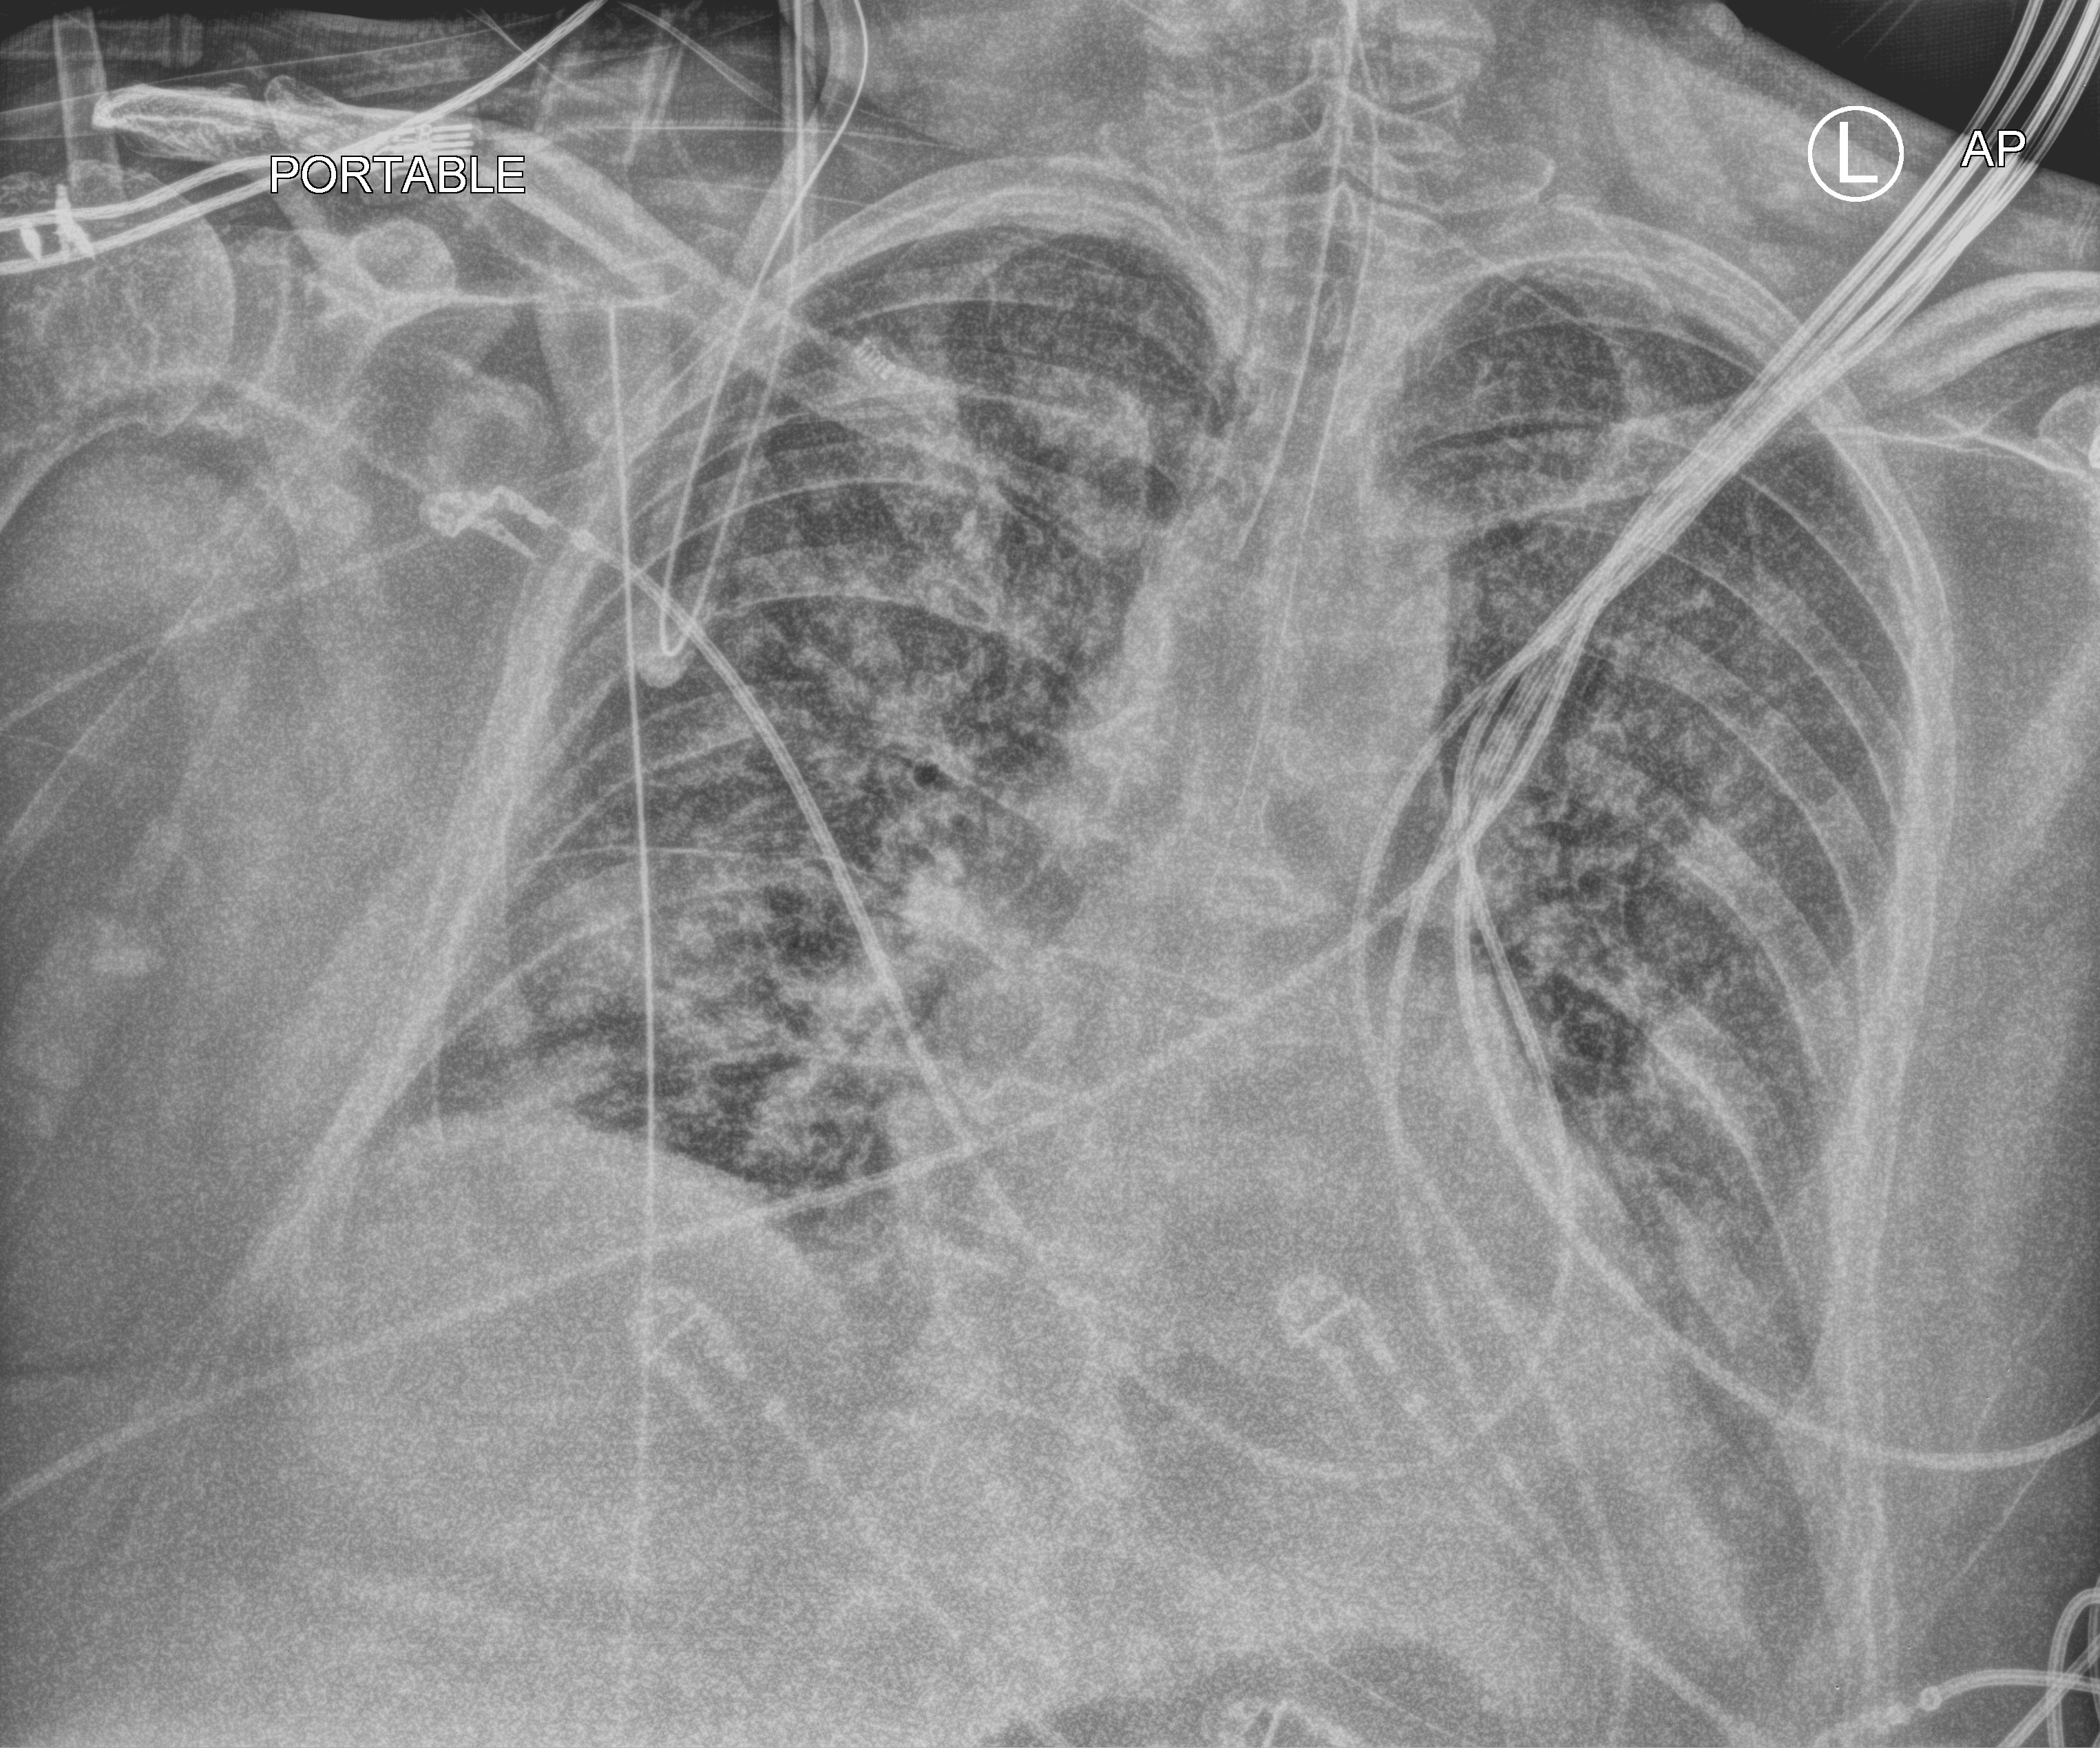
Bedside chest radiograph (computed radiography), anteroposterior (AP) projection. Patient hospitalised with COVID-19; male, aged 60–74 years.
Hospital-stay facts (about this admission, not read from this image; timing relative to this image not recorded):
- mechanically ventilated during this hospital stay: yes